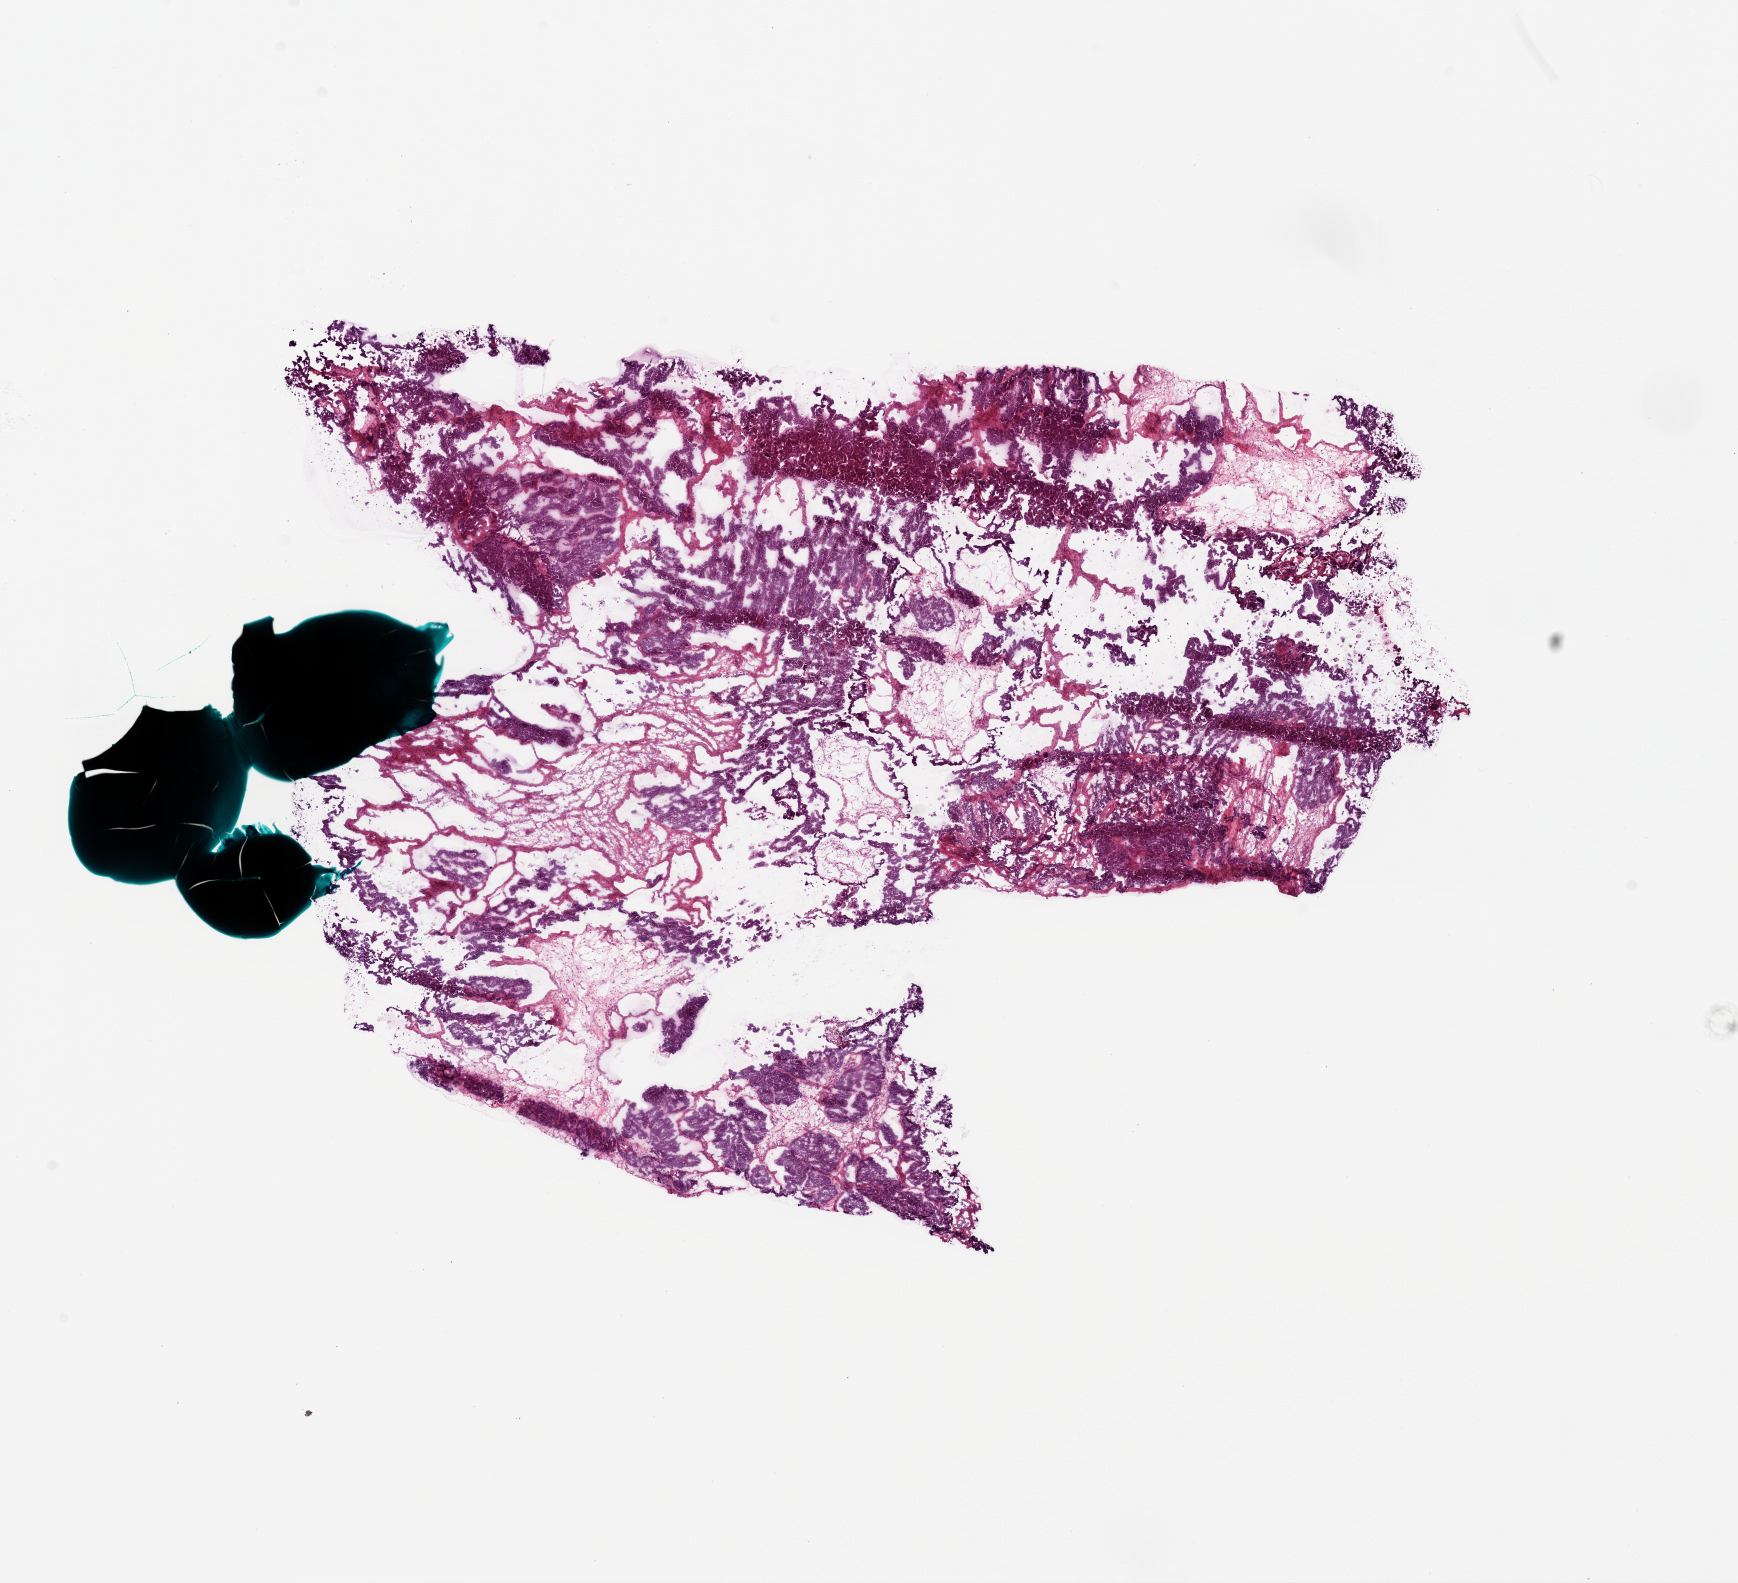
Whole-slide histology image, H&E-stained, whole scanned area (about 14.0 x 12.8 mm, from a 20x scan) shown as a low-resolution overview. Frozen section. Sample: primary tumour, ovary. Patient: female, age at initial diagnosis 80 years. Histologic grade: G3 (poorly differentiated). Slide review estimates, as recorded: tumour cells 70%, tumour nuclei 85%, normal cells 10%, stromal cells 20%, necrosis 0%.
FIGO stage: IIIC. Pathologic diagnosis: Serous cystadenocarcinoma, NOS.